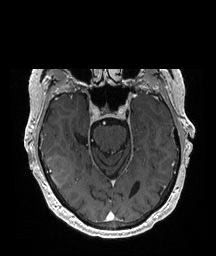
Brain MRI from a brain-tumour surgery series, one axial slice; position 137 of 208 along the scan axis; T1-weighted post-contrast; 1 mm slice thickness; 216 × 256 image matrix, field of view 216 × 256 mm. From the clinical record (not read from this slice): histopathology: Glioblastoma; WHO grade: 4; IDH mutation: no.
Annotated regions visible in this slice (outlined manually by an expert reader):
- tumour: bounding box [x1, y1, x2, y2] px = [46, 155, 72, 188]